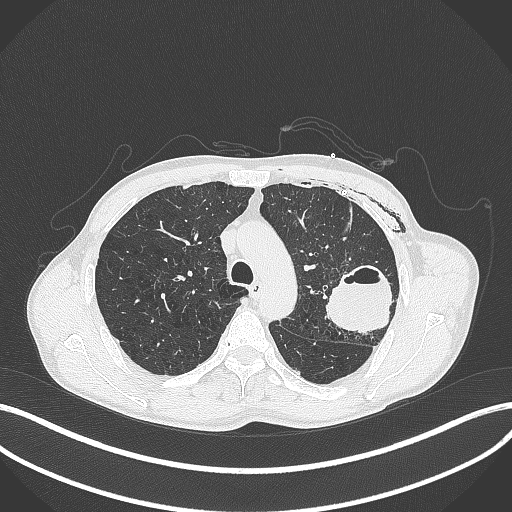
Chest CT, one axial slice; slice 291 of 457 in the series (ordered by position); reconstruction kernel B70f; lung window (W 1500 / L -600 HU); 1 mm slice thickness; 512 × 512 image matrix, field of view 400 × 400 mm. Patient: male, 58 years. From the clinical record (not read from this slice): clinical TNM (as recorded): T3 N0 M0.
Structures marked on this image (bounding box drawn by a radiologist):
- lung tumour (recorded histology: adenocarcinoma): box from (x=323, y=258) to (x=397, y=339) px